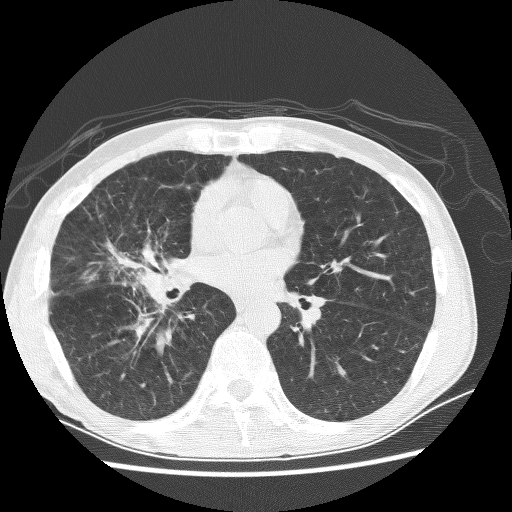
Axial slice from a low-dose chest CT screening exam; first (baseline) screen; lung window (W 1500 / L -600 HU); lung (sharp) reconstruction kernel (BONE); slice 131 of 256 in the series. Male participant, aged 67 years at enrolment.
Expert reader's lesion annotation, bounding box (x1, y1, x2, y2) in pixels: (74, 227, 173, 302). The exam's reader record, not a measurement of the box and not confirmed to be the same lesion: non-calcified nodule or mass ≥4 mm, right middle lobe, 28 × 18 mm, spiculated (stellate) margins, soft tissue attenuation.